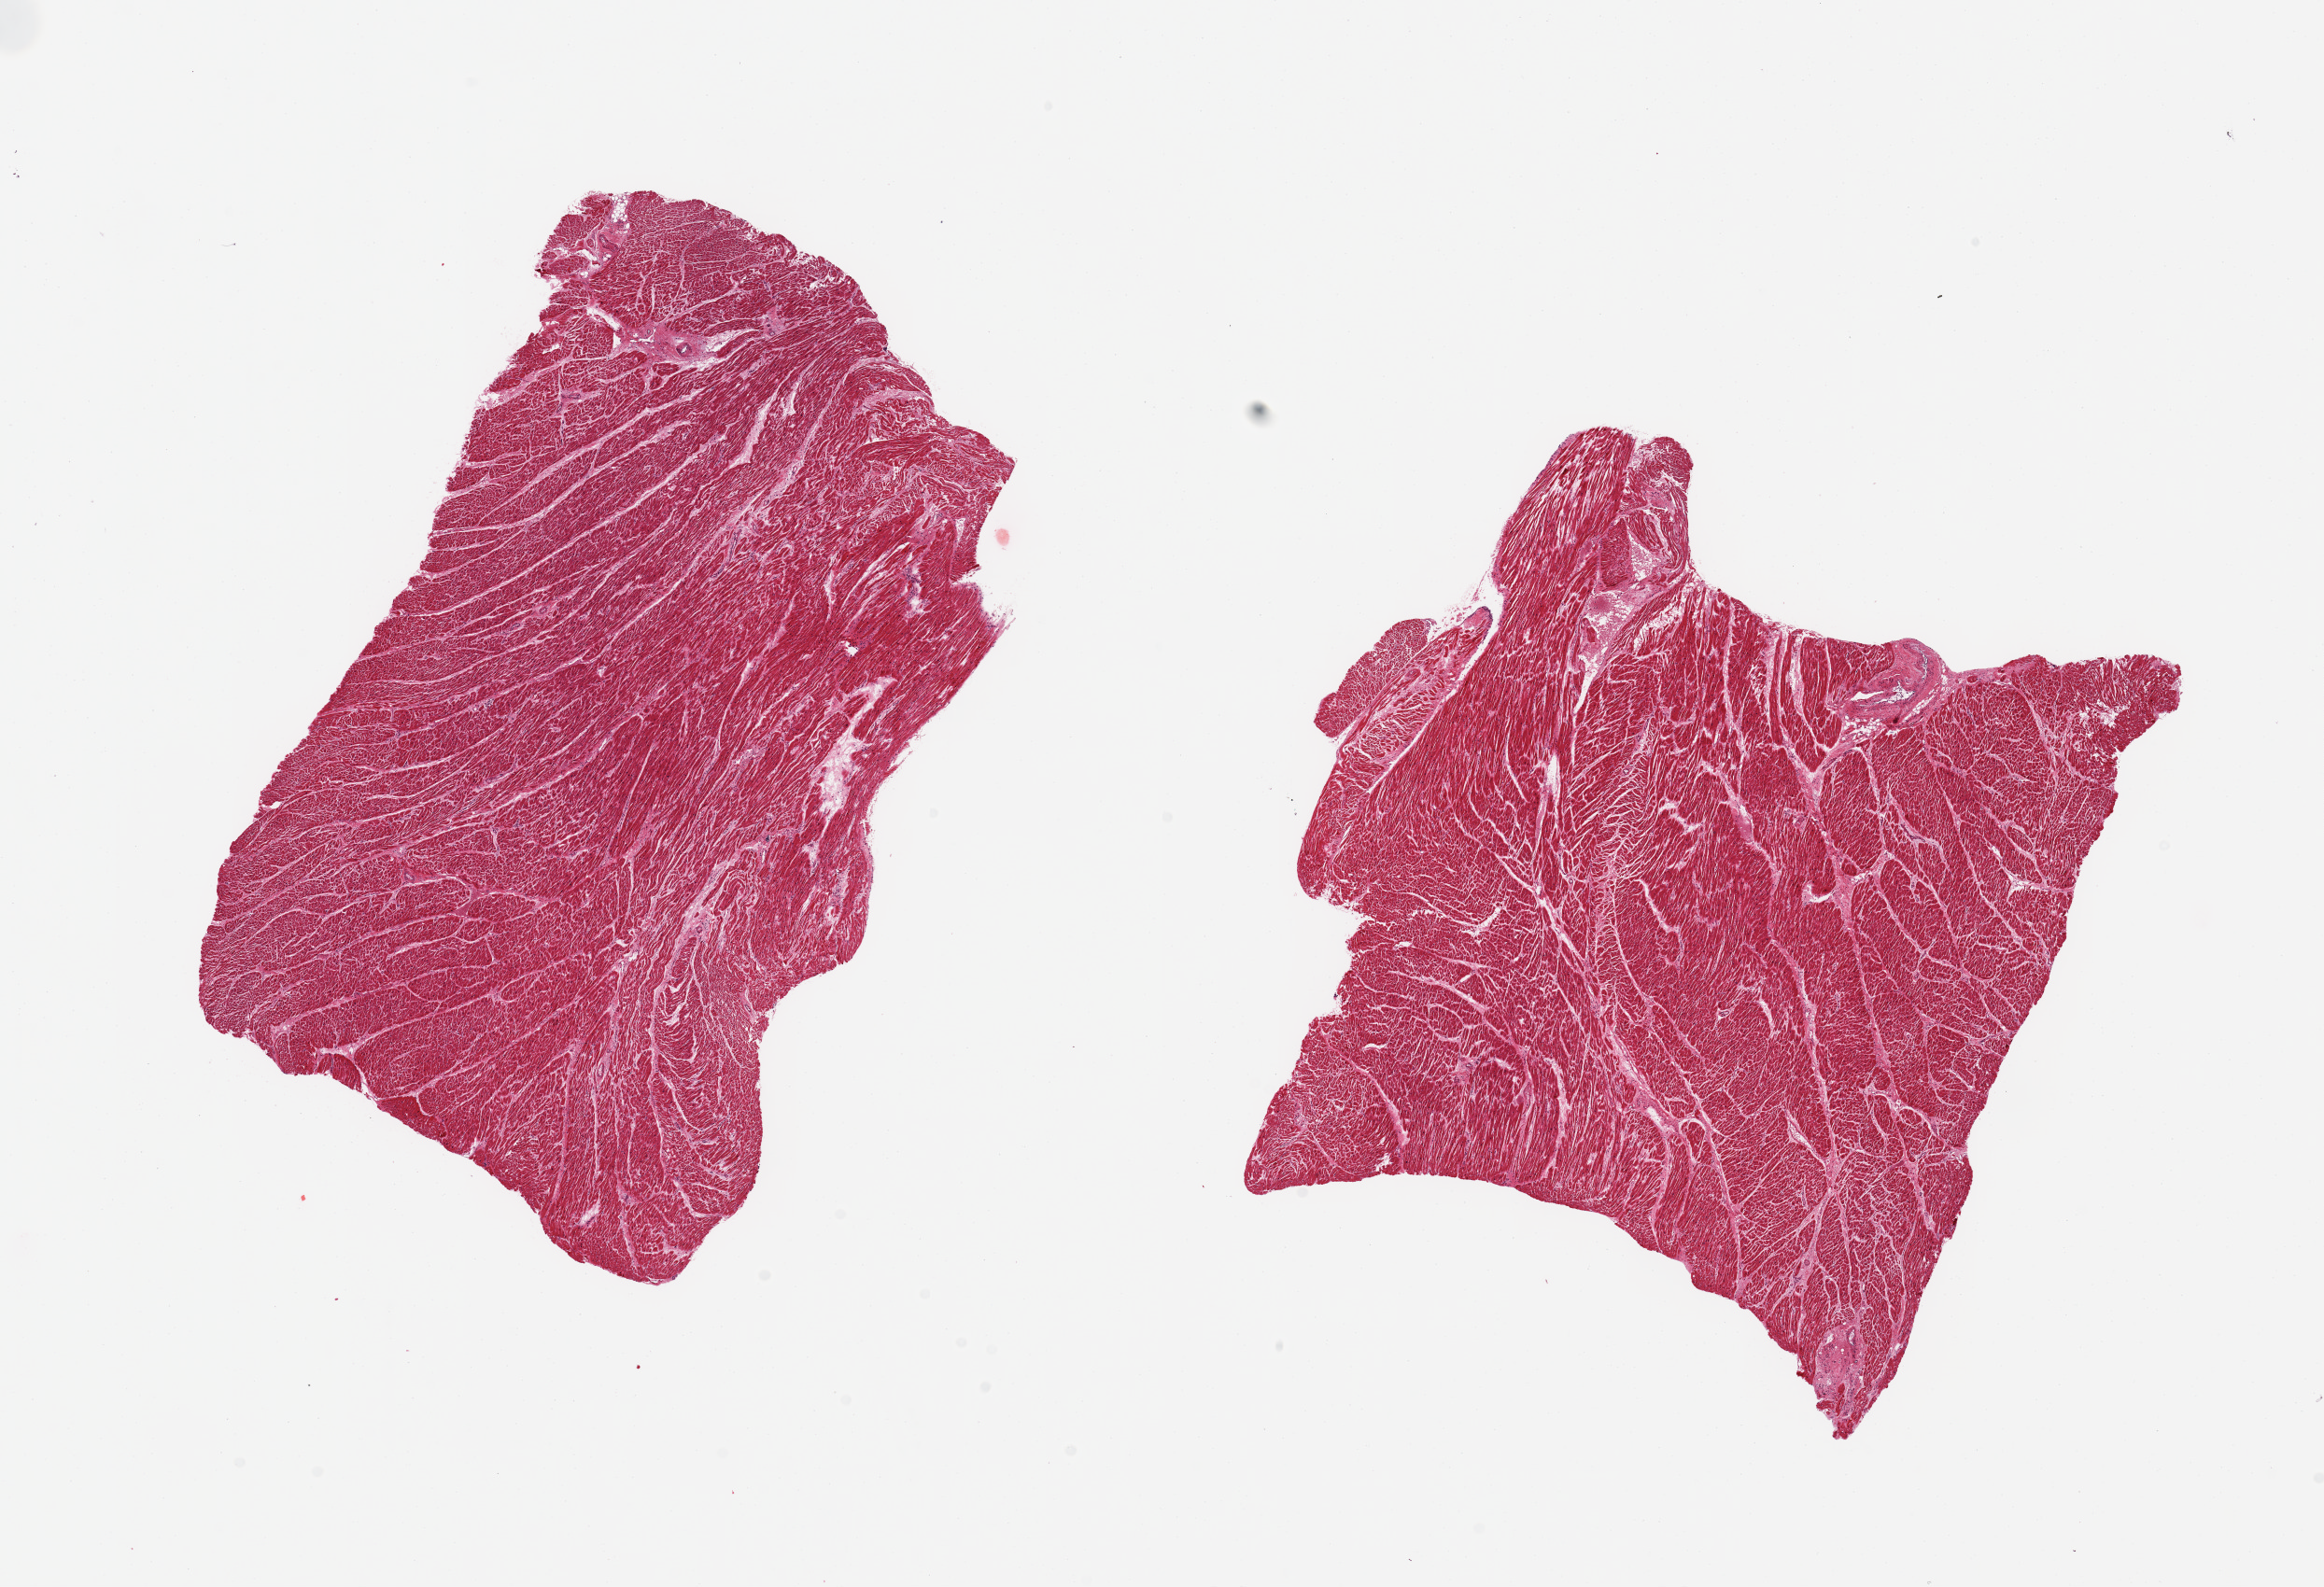
Haematoxylin and eosin whole-slide image — a low-resolution overview of the entire scanned area, about 19.7 x 13.4 mm, PAXgene-fixed, paraffin-embedded tissue, sampled site (target tissue): heart, tissue donor sample. Donor sex: male.
Reviewer comment on this tissue sample: 2 pieces ~7.8x6 mm.